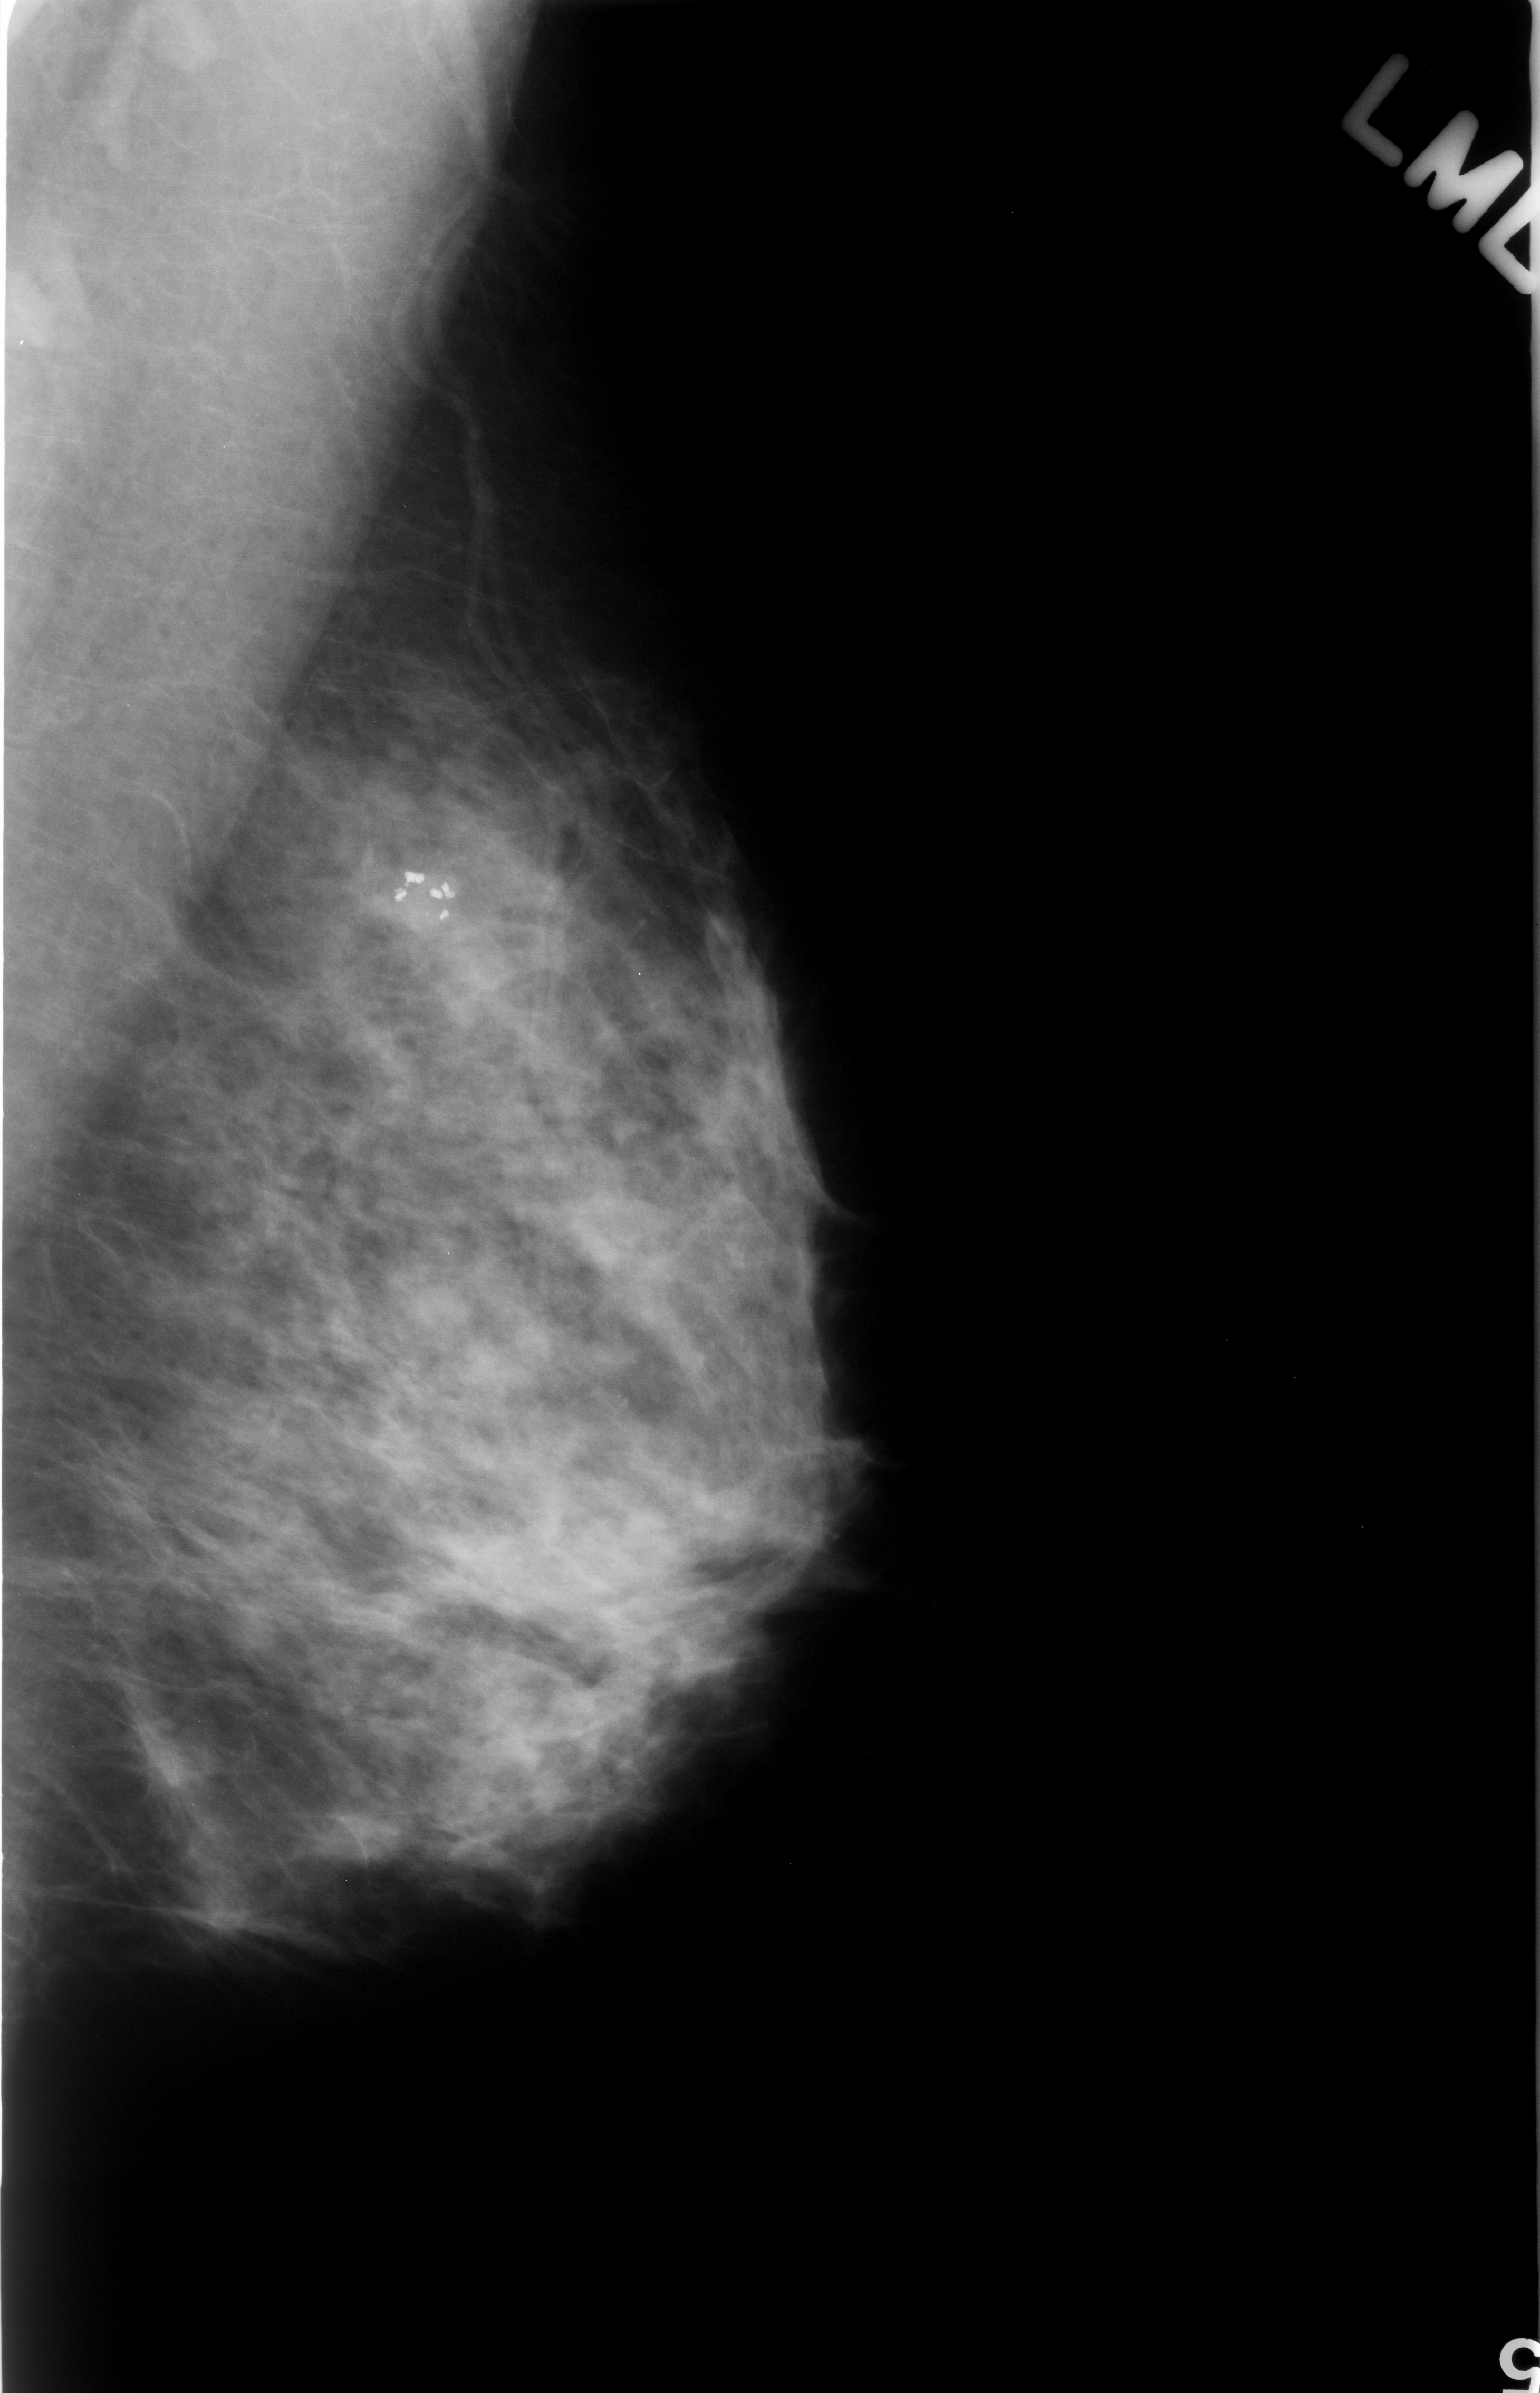
Digitized screen-film mammogram; left breast; MLO view.
Finding: calcifications, morphology dystrophic, distribution clustered; BI-RADS assessment category 2; benign without callback (not worked up further).